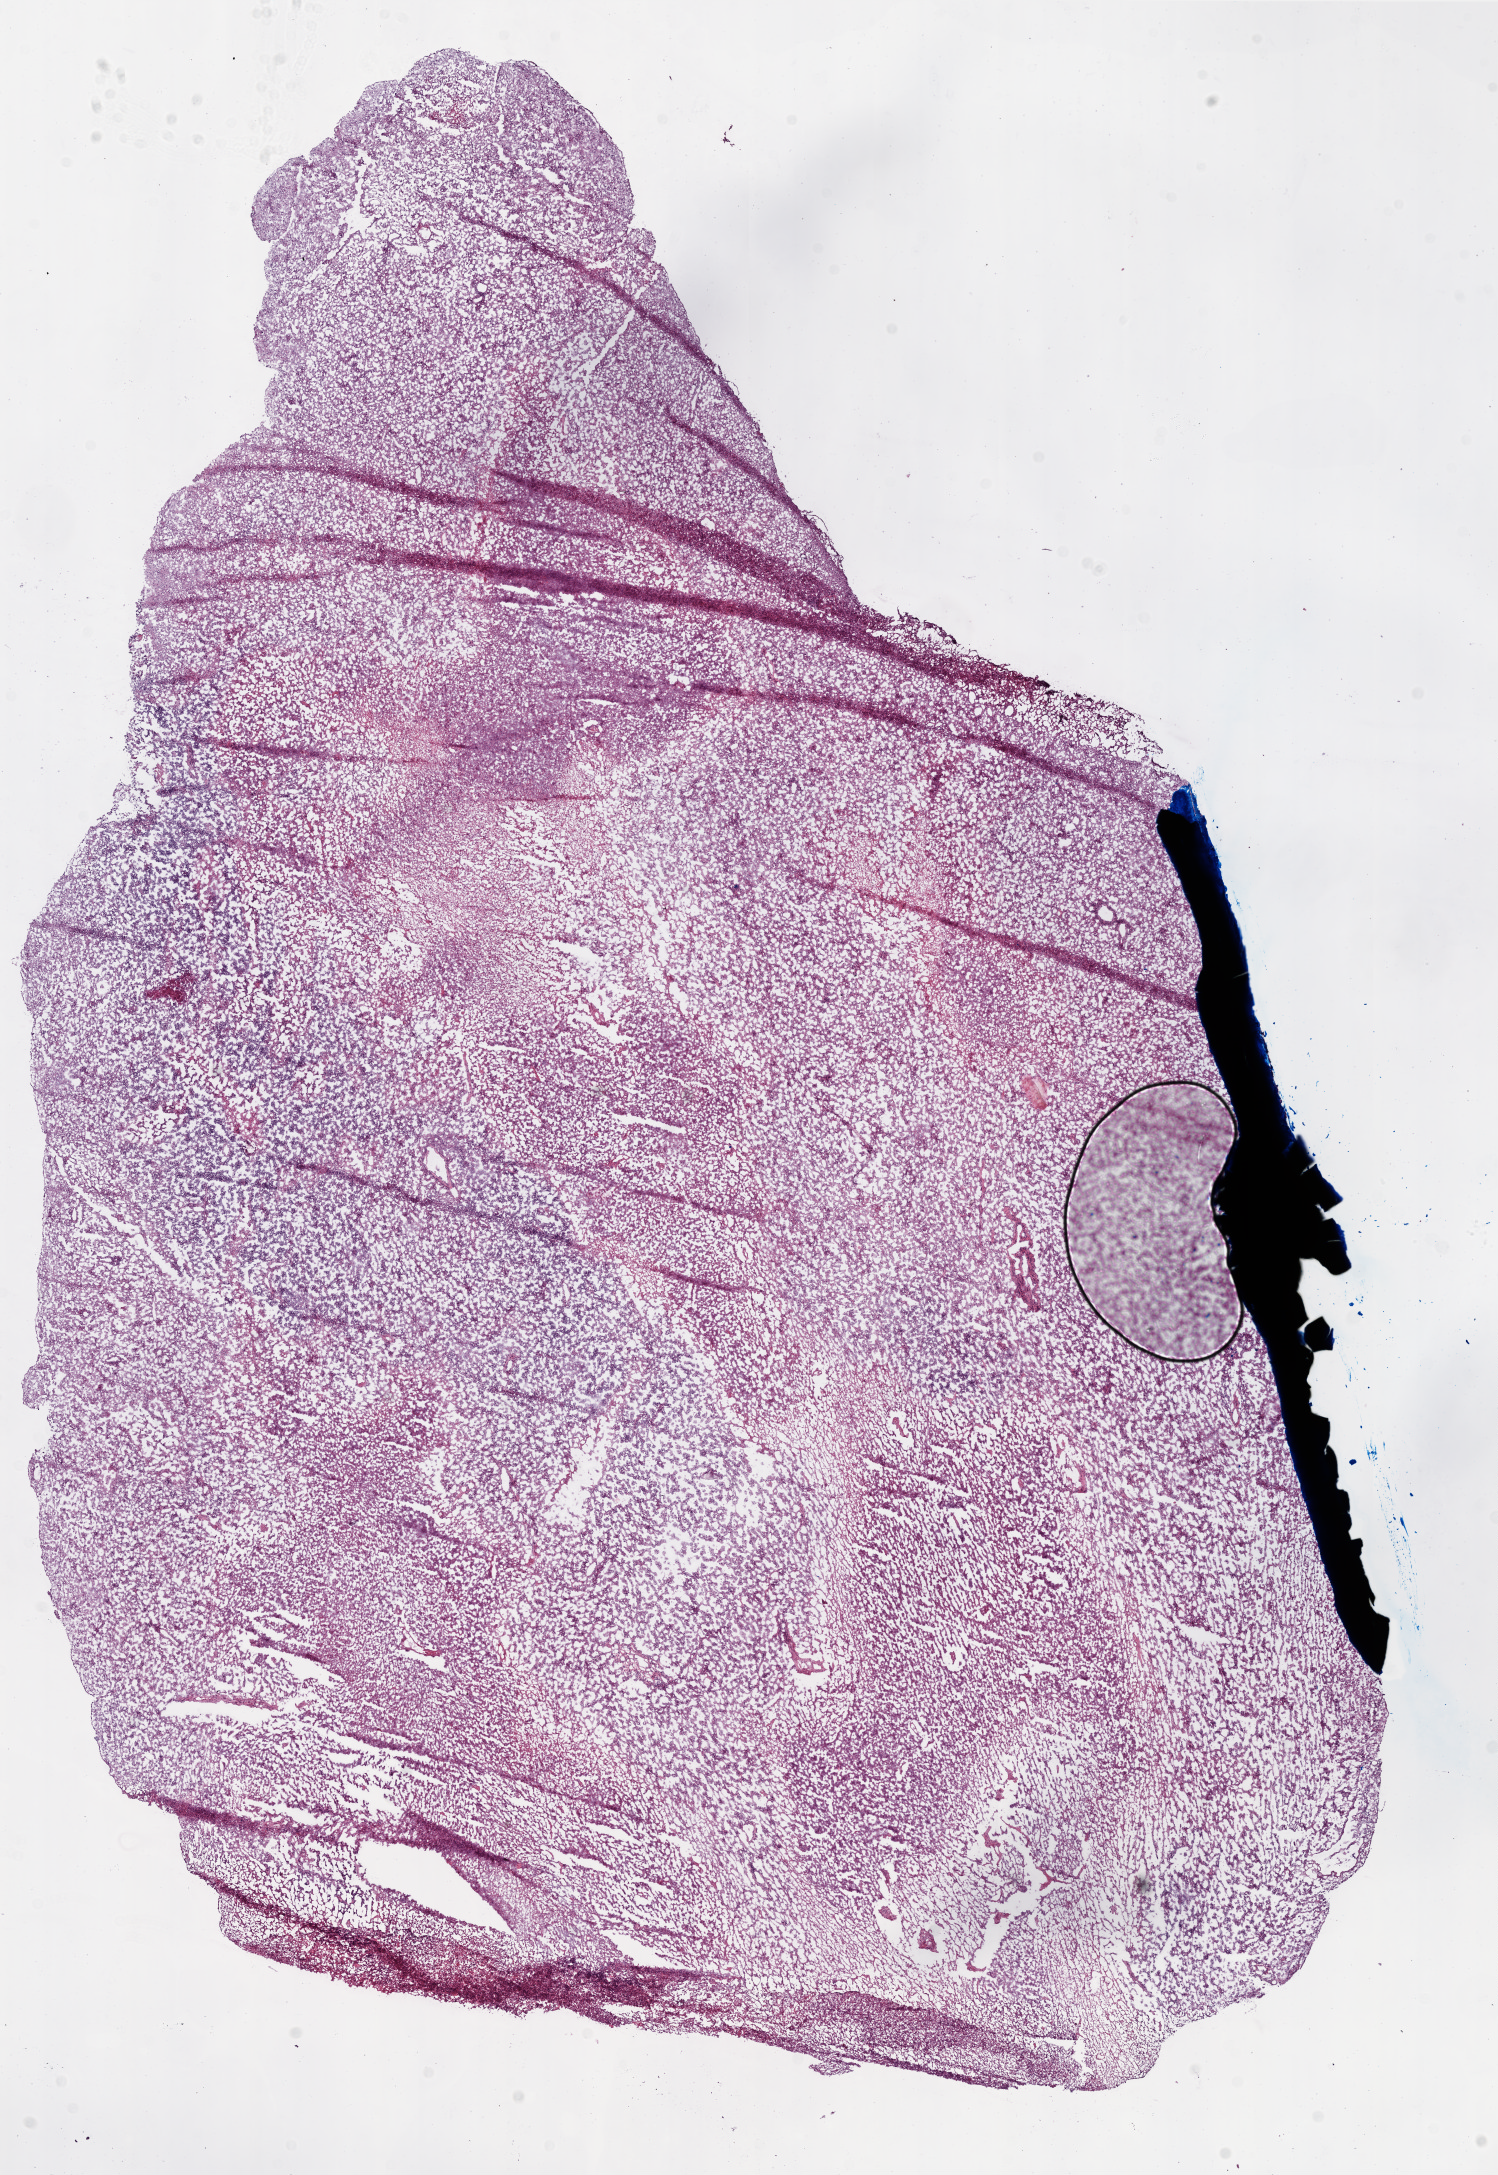
Digitized Hematoxylin and eosin (H&E) stained tissue section (whole slide), low-resolution overview of the scanned area, about 12.0 x 17.4 mm (from a 20x scan). Frozen section from the top of the tissue portion. Brain, primary tumour sample. Patient: male, age at initial diagnosis 74 years.
Histologic diagnosis: Glioblastoma.